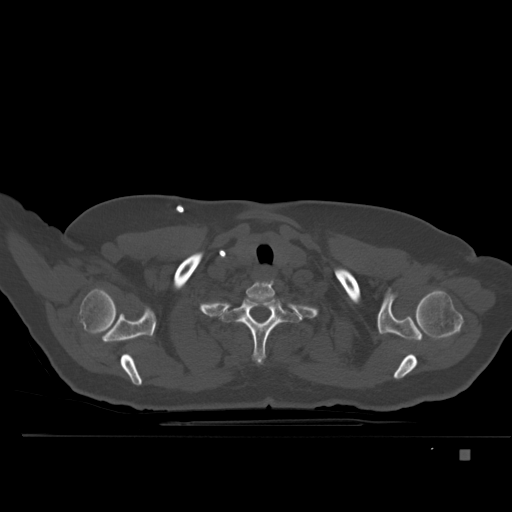
CT including the spine, one axial slice; position 403 of 477 along the scan axis; bone window (W 1800 / L 400 HU); 512 × 512 image matrix, field of view 422 × 422 mm. Female patient, age 74 years. Case-level facts recorded for this patient, not image findings: primary cancer: colon.
Structures marked on this image (semi-automatically segmented with operator editing):
- T1 vertebra: bounding box [x1, y1, x2, y2] px = [233, 295, 286, 363]